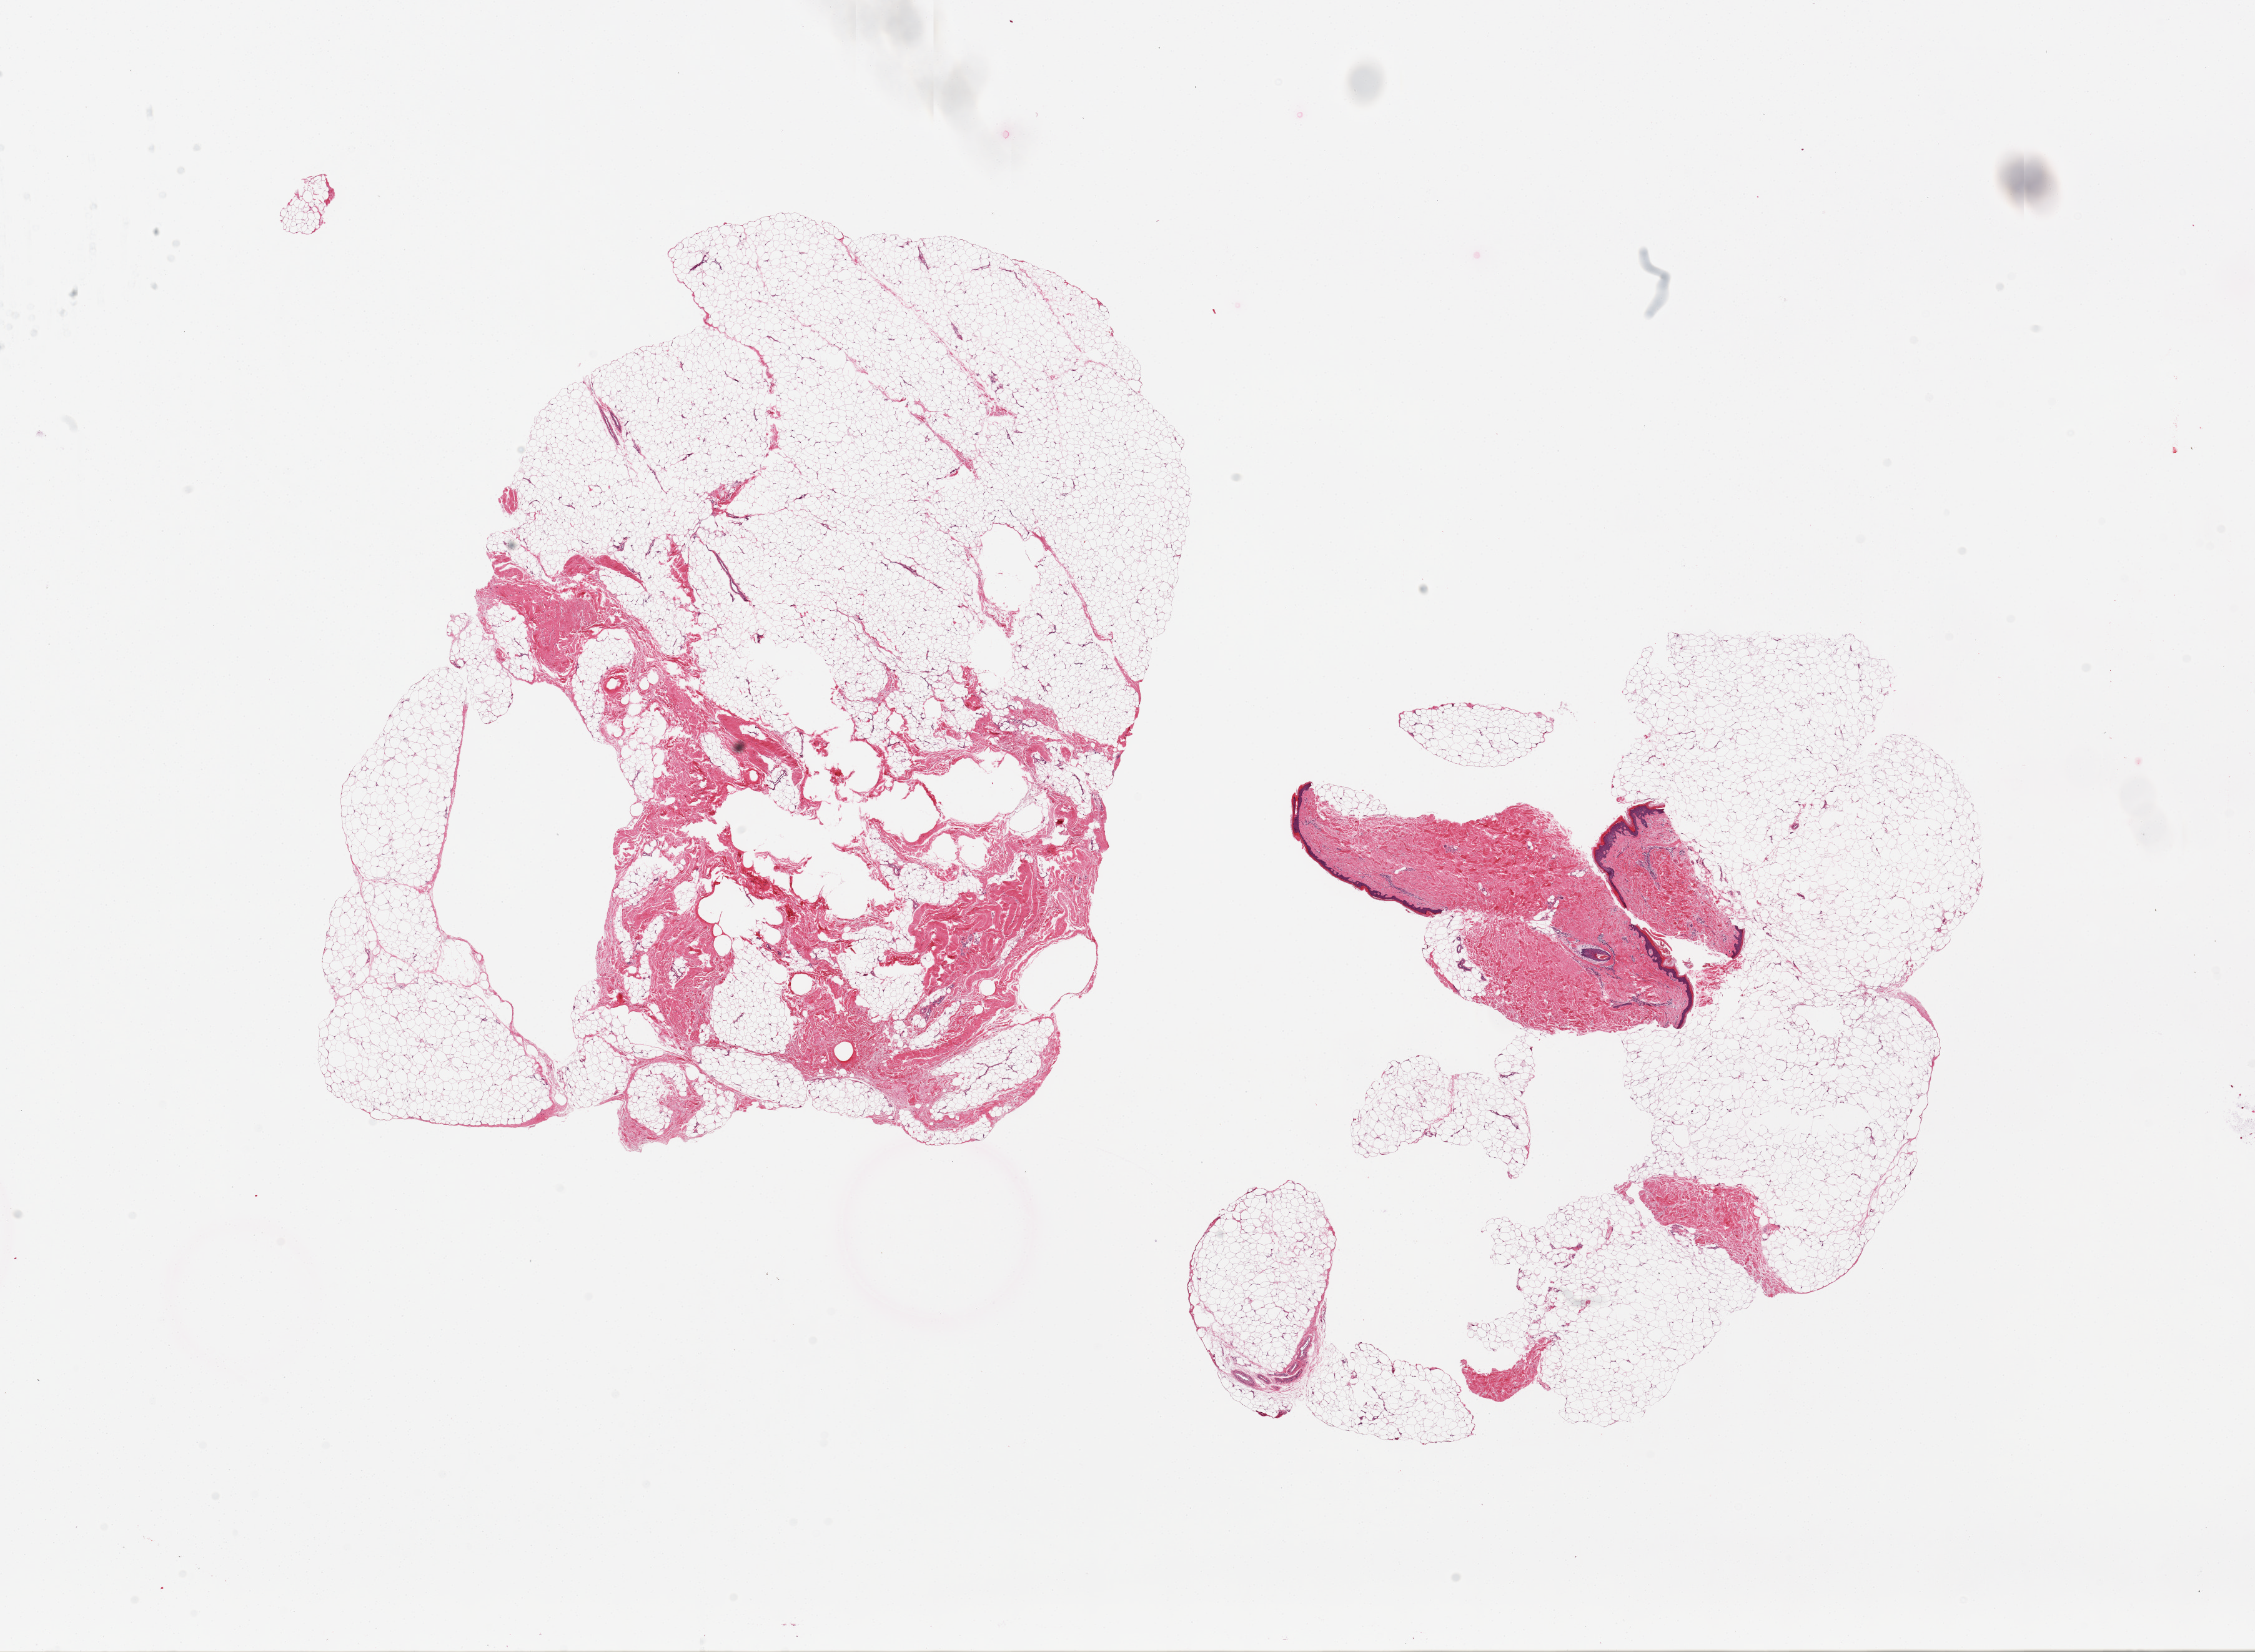
Whole-slide image, hematoxylin and eosin (H&E) stain — shown as a low-resolution overview of the whole scanned area (about 28.5 x 20.9 mm), PAXgene-fixed, paraffin-embedded tissue, sampled site (target tissue): adipose tissue, donor tissue sample. Male donor.
Pathologist's review note for this sample: 2 pieces, 12x8.5 and 12x9mm; fibrofatty tissue in one, skin and fatty tissue in other.